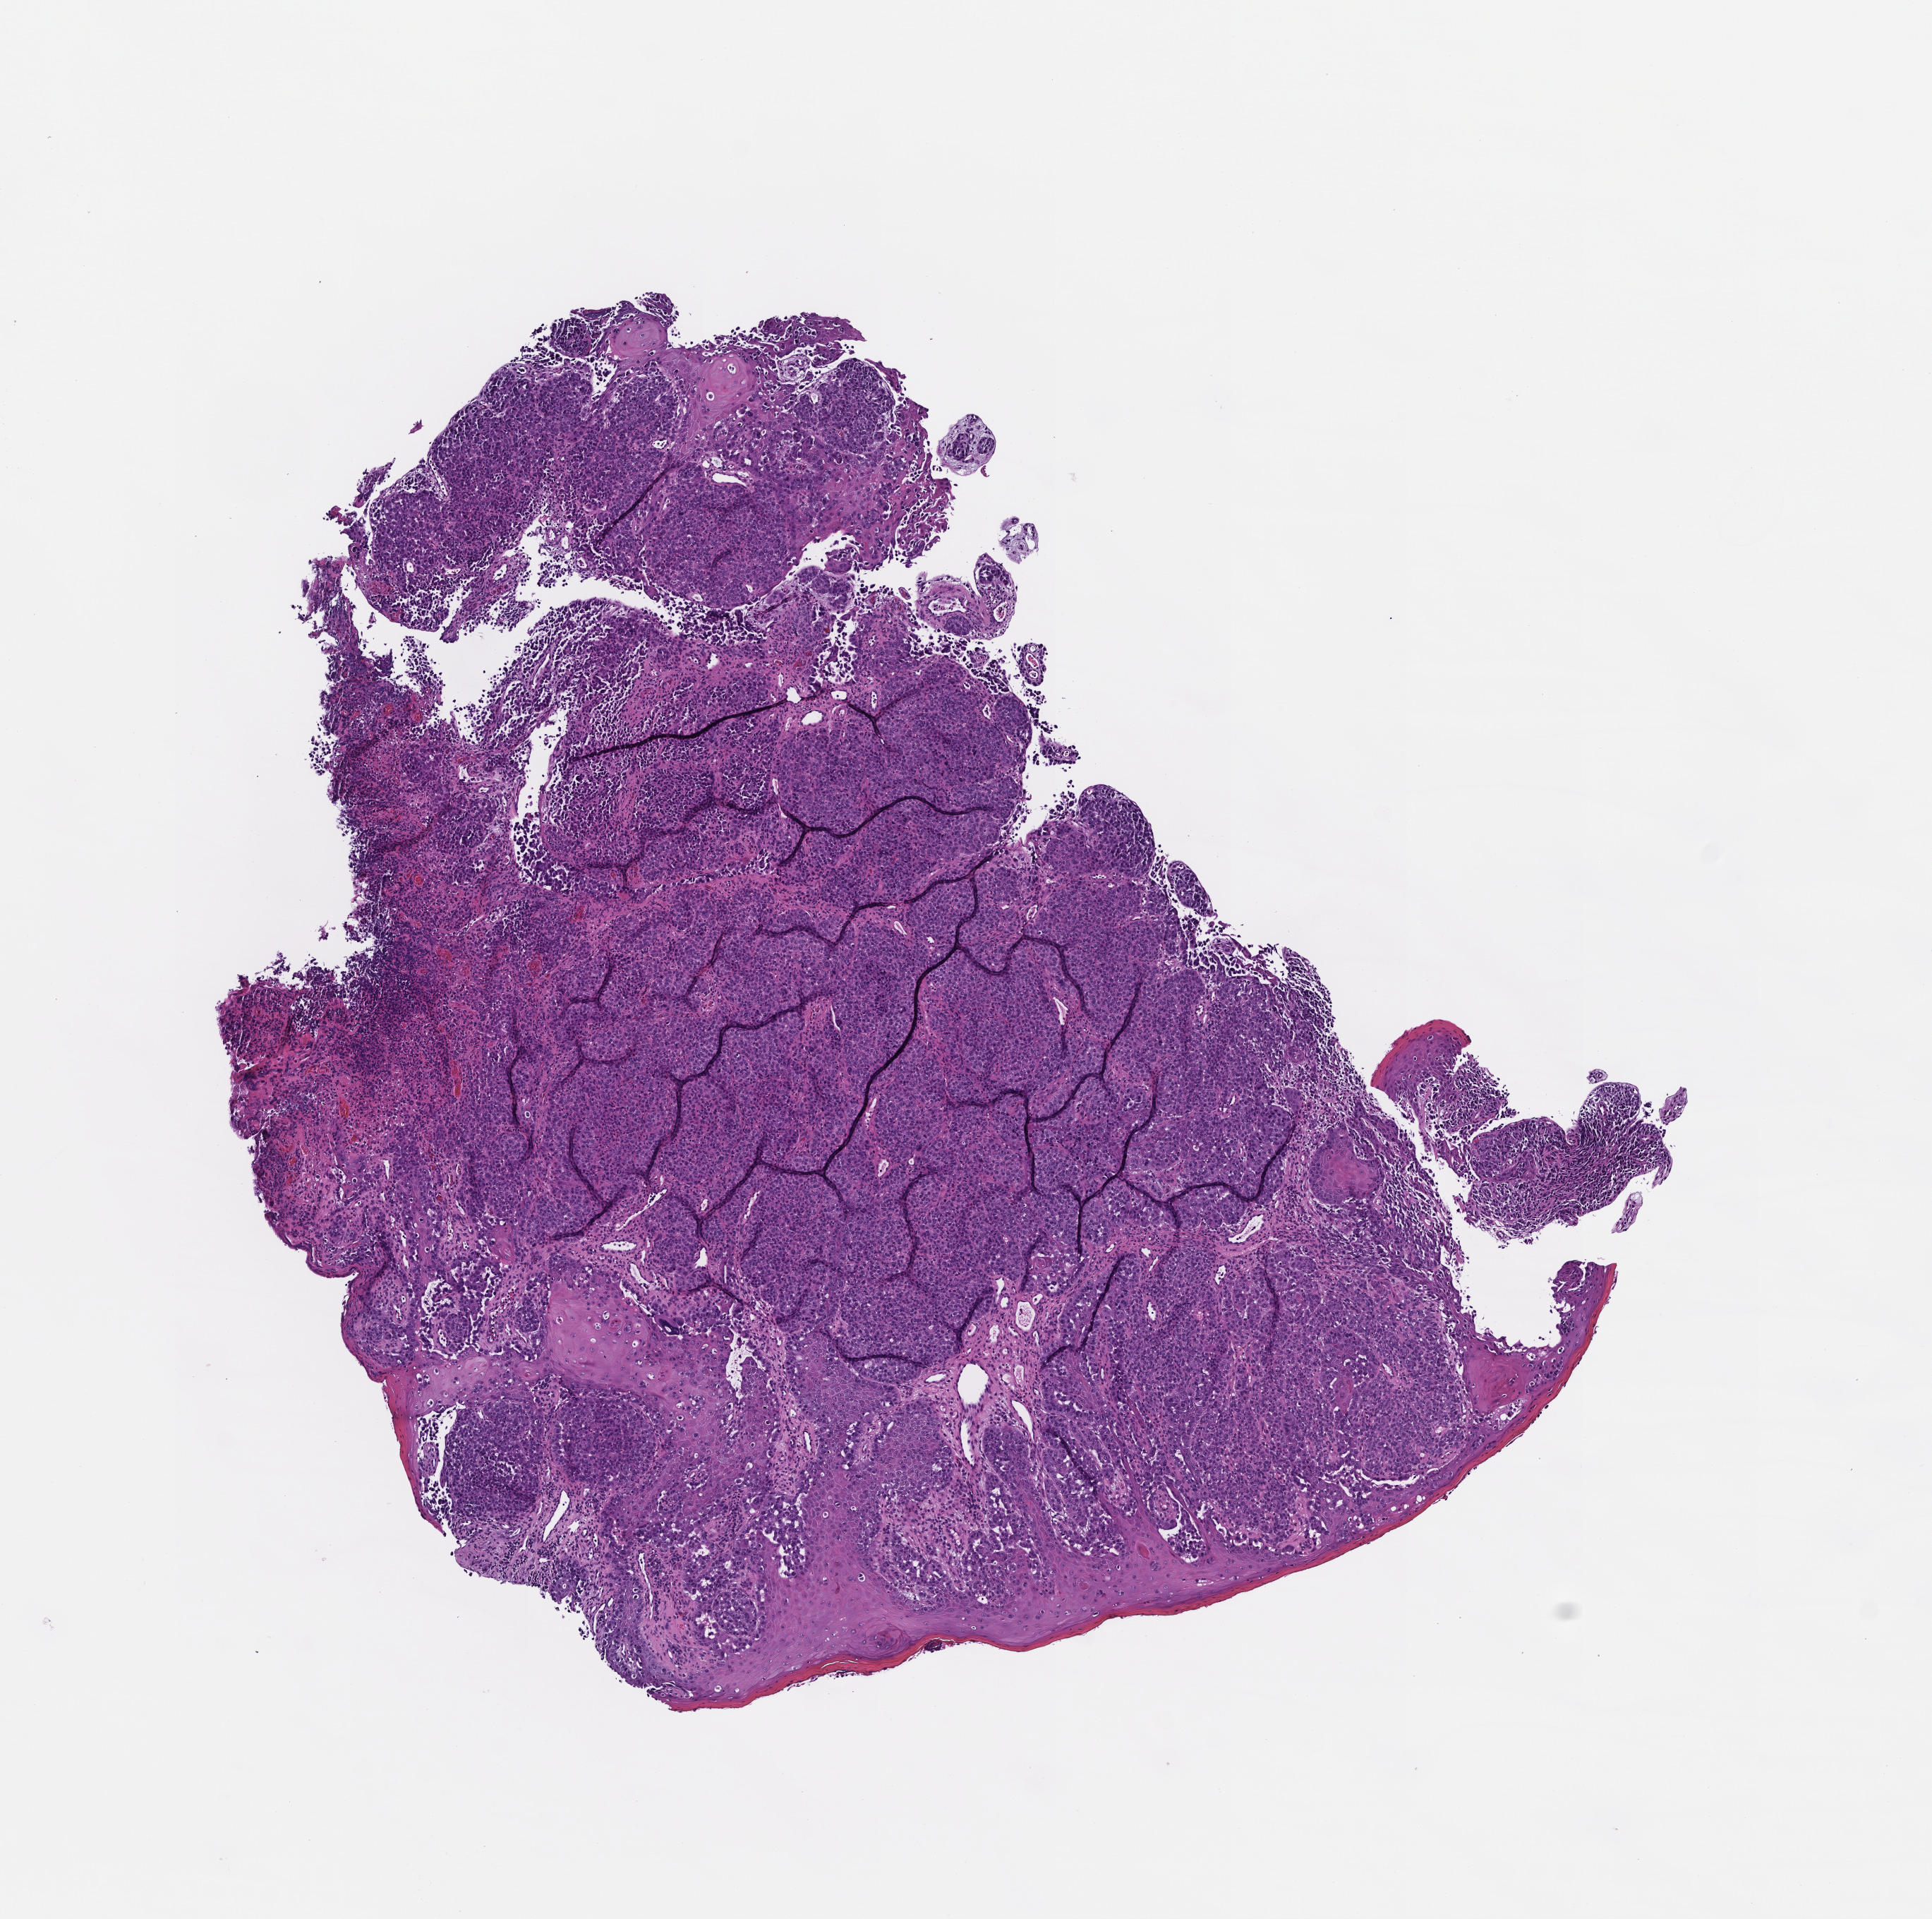
Whole-slide image, H&E stain — whole scanned area (about 5.5 x 5.5 mm) shown as a low-resolution overview; formalin-fixed, paraffin-embedded (FFPE) tissue; site: skin. Patient sex: male.
This section: primary tumour tissue. Diagnosis: Melanoma.